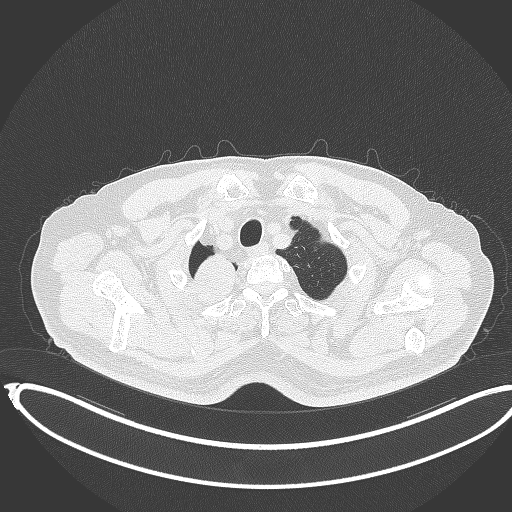
Chest CT, one axial slice; slice 337 of 403 in the series (ordered by position); reconstruction kernel B70f; lung window (W 1500 / L -600 HU); 1 mm slice thickness; 512 × 512 image matrix. Patient: male, 68 years. Case-level facts recorded for this patient, not image findings: clinical TNM (as recorded): T2a N0 M0.
Outlined on this slice (bounding box drawn by a radiologist):
- lung tumour (recorded histology: adenocarcinoma): box from (x=186, y=251) to (x=238, y=302) px